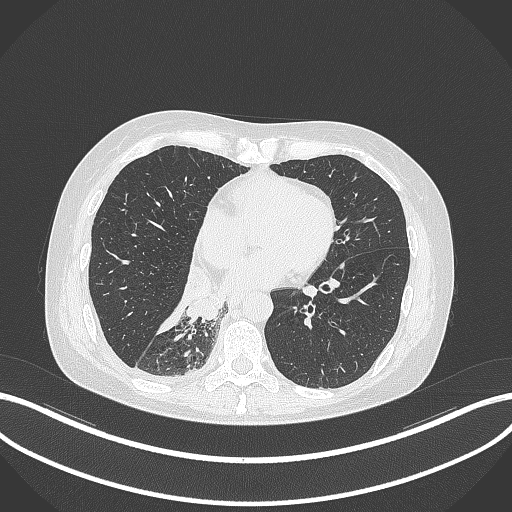
Chest CT, one axial slice; position 118 of 329 along the scan axis; 120 kVp; lung window (W 1500 / L -600 HU); 1 mm slice thickness; 512 × 512 image matrix, field of view 400 × 400 mm. Female patient, age 63 years. Case-level facts recorded for this patient, not image findings: clinical TNM (as recorded): T1c N0 M0.
Annotated regions visible in this slice (rectangle marked by the reading radiologist):
- lung tumour (recorded histology: adenocarcinoma): bounding box (x1, y1, x2, y2) in pixels: (178, 270, 219, 324)